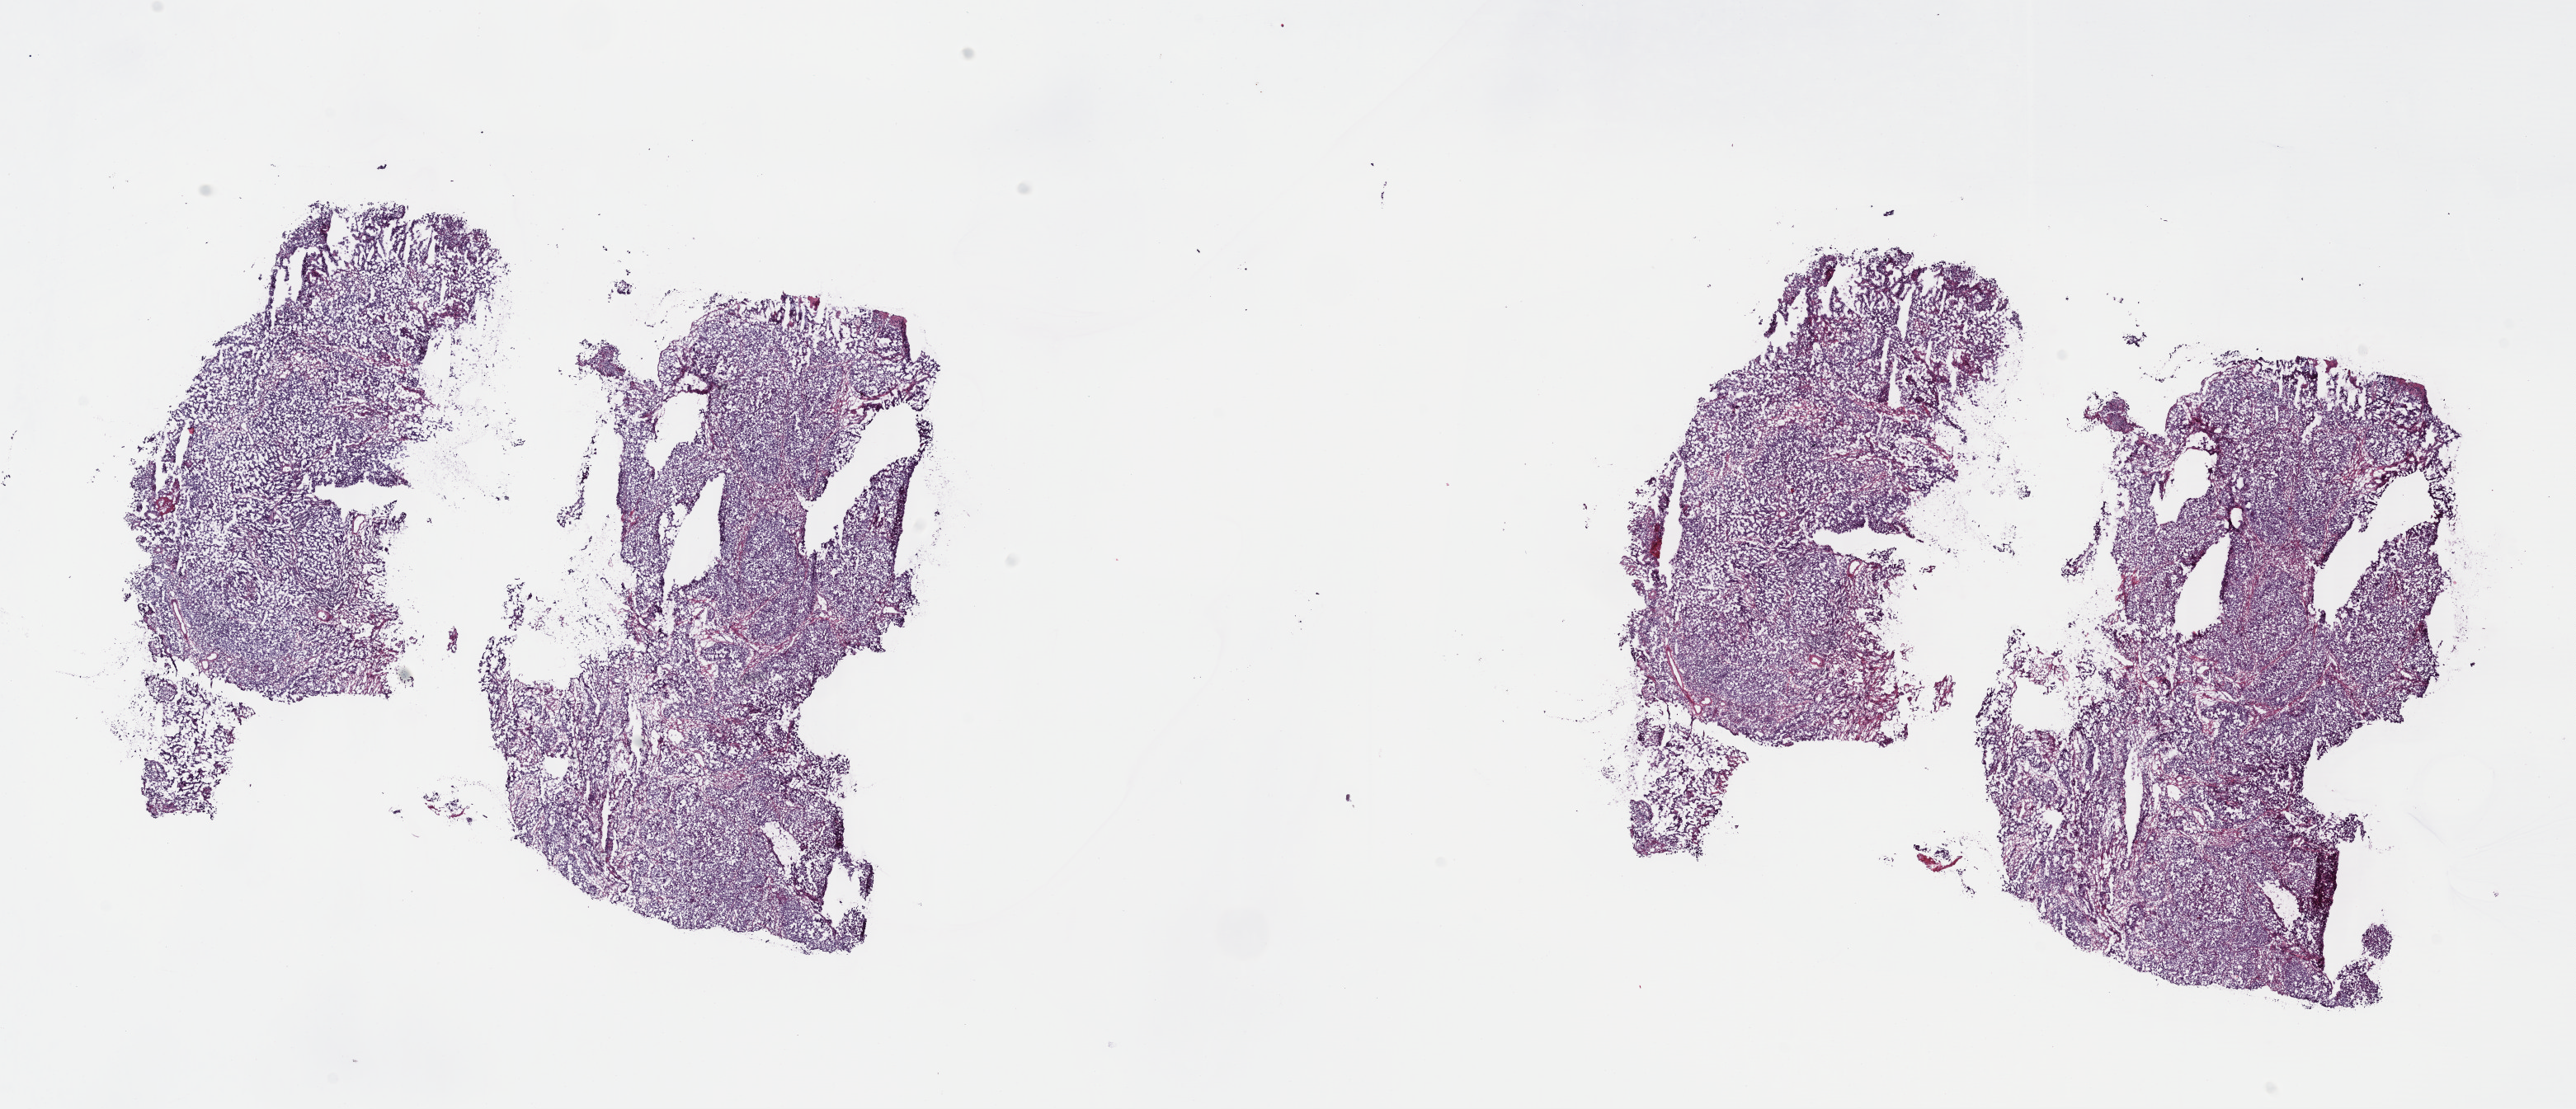
Whole-slide histology image, H&E-stained — shown as a low-resolution overview of the whole scanned area (about 24.6 x 10.6 mm). Frozen section from the top of the tissue portion. Sample: primary tumour, bladder. Patient: male, age at initial diagnosis 56 years. Histologic grade: high grade. Pathologist review of this section (percent, as recorded): tumour cells 100%, tumour nuclei 80%, normal cells 0%, stromal cells 0%, necrosis 0%. Inflammatory infiltration, as recorded: lymphocyte infiltration 3%, monocyte infiltration 0%, neutrophil infiltration 0%.
AJCC pathologic stage: II (7th edition). TNM: T2b NX M0. Histologic diagnosis: Papillary transitional cell carcinoma.